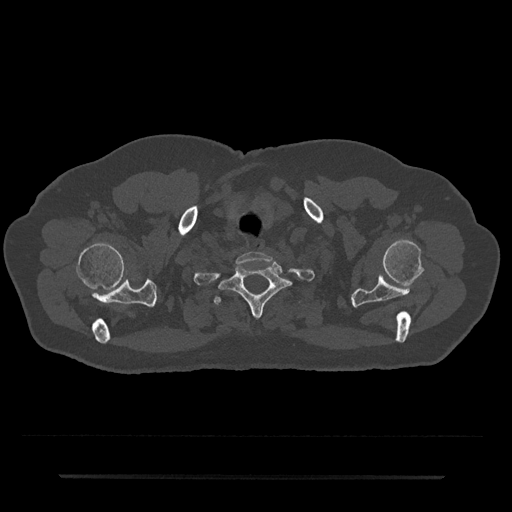
CT including the spine, one axial slice; slice 641 of 797 in the series (ordered by position); bone window (W 1800 / L 400 HU); 0.5 mm slice thickness; 512 × 512 image matrix. Male patient, age 69 years. From the clinical record (not read from this slice): primary cancer: prostate.
Structures marked on this image (semi-automatically segmented with operator editing):
- T1 vertebra: bounding box <218,263,298,317> (left, top, right, bottom; pixels)
- T2 vertebra: <214,295,300,305>